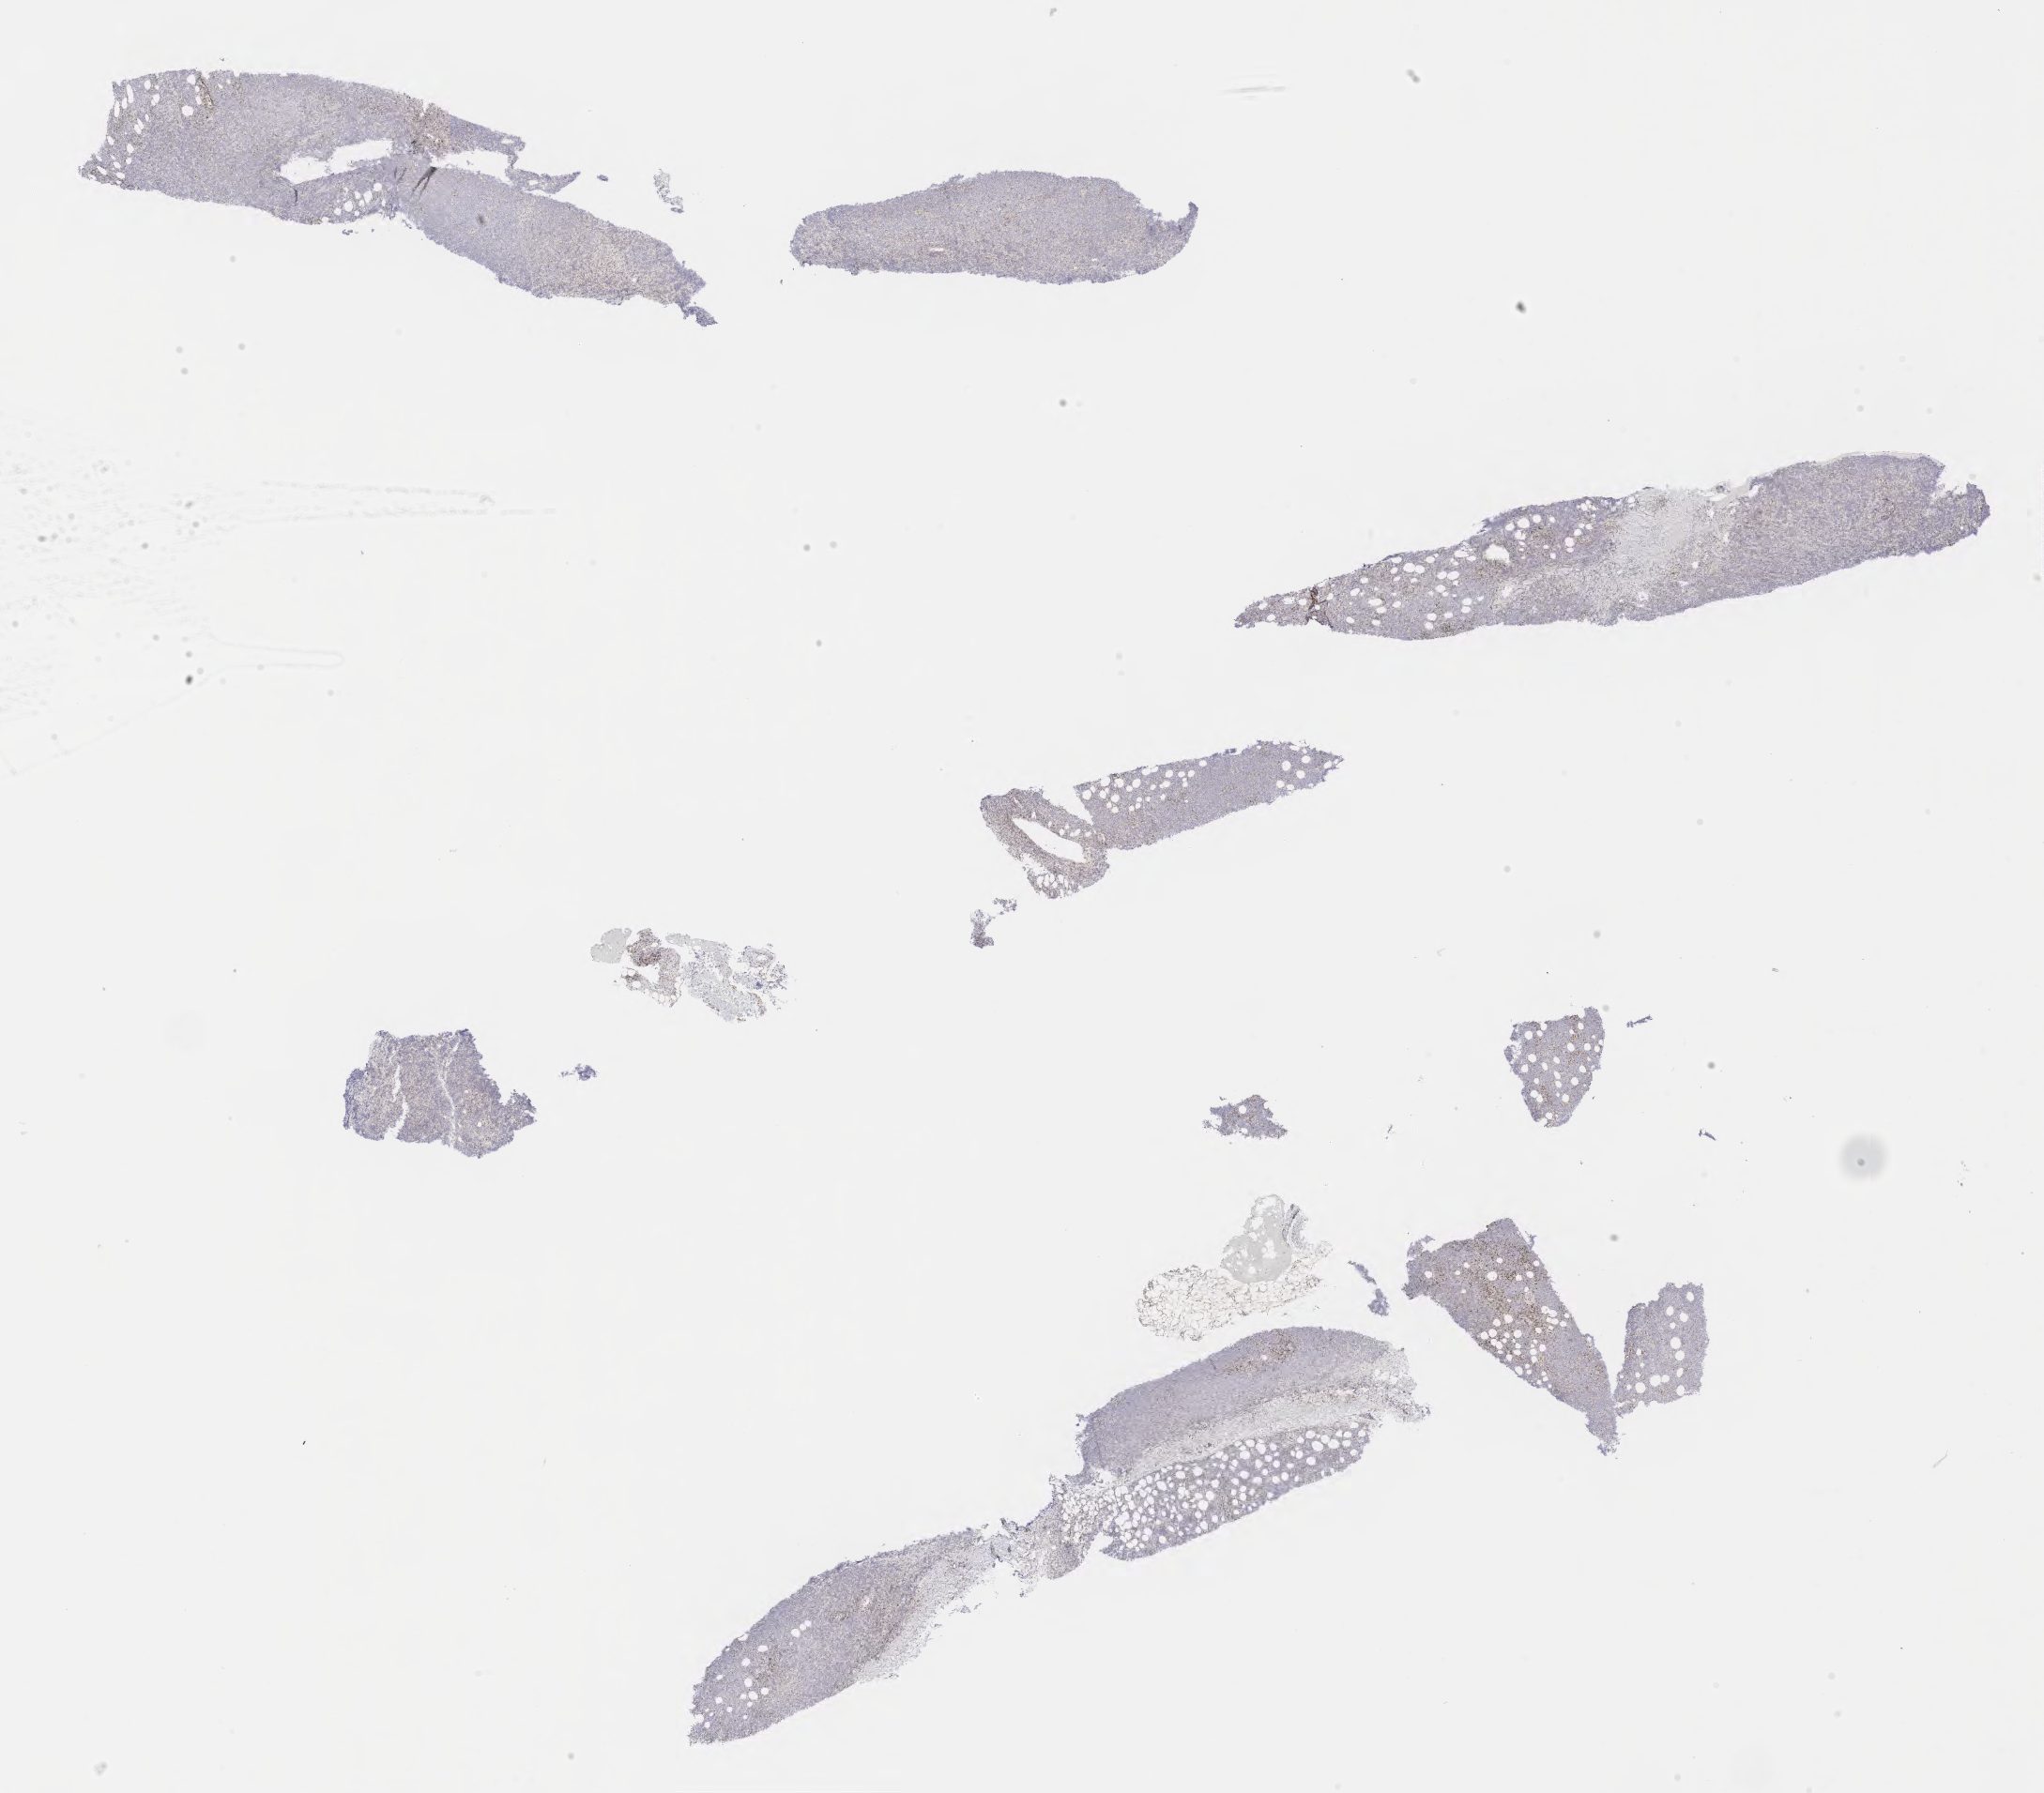
IHC for BCL2, whole-slide image — shown as a low-resolution overview of the whole scanned area (about 17.6 x 15.5 mm). Specimen: tumor tissue. Patient: male, 33 years old.
- diagnosis: Burkitt lymphoma, NOS